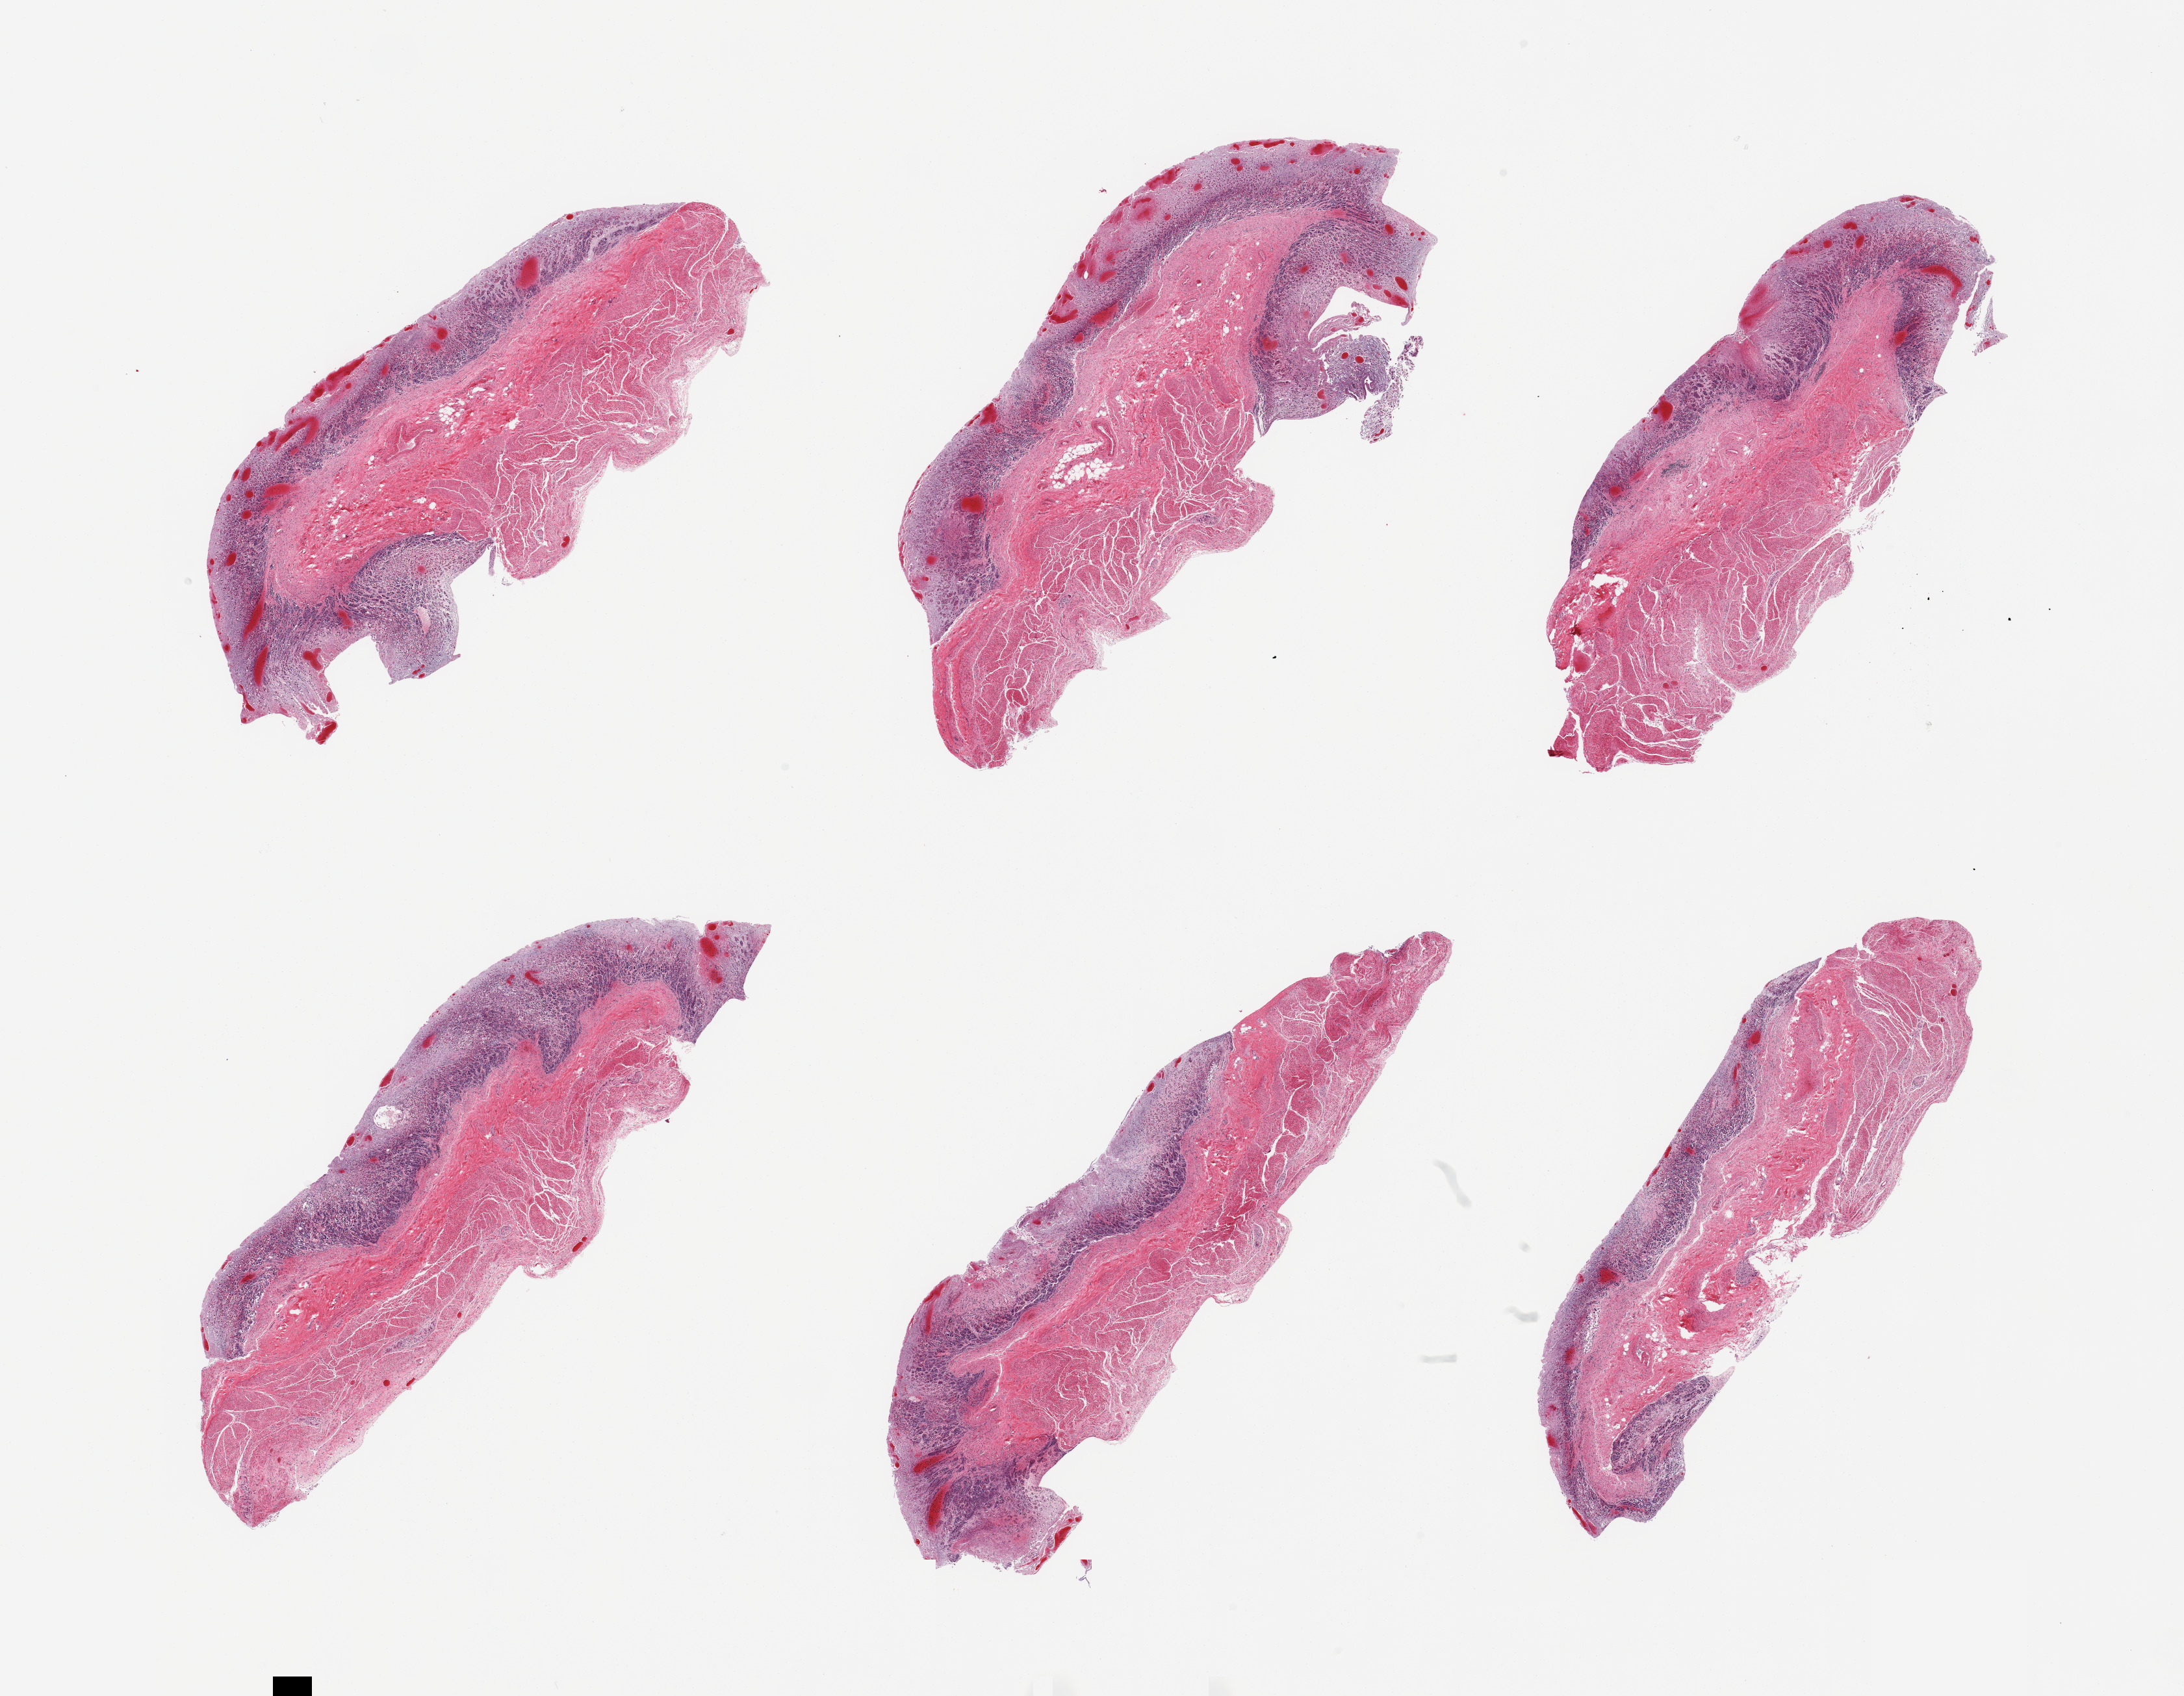
Digitized H&E-stained section — low-resolution overview of the scanned area, about 26.6 x 20.6 mm; PAXgene-fixed, paraffin-embedded tissue; target tissue: stomach; donor tissue sample. Donor: male.
Review note (as recorded): 6 pieces mucosa up to ~0.8mm, ~25% thickness, advanced glandular mucosal autolysis.